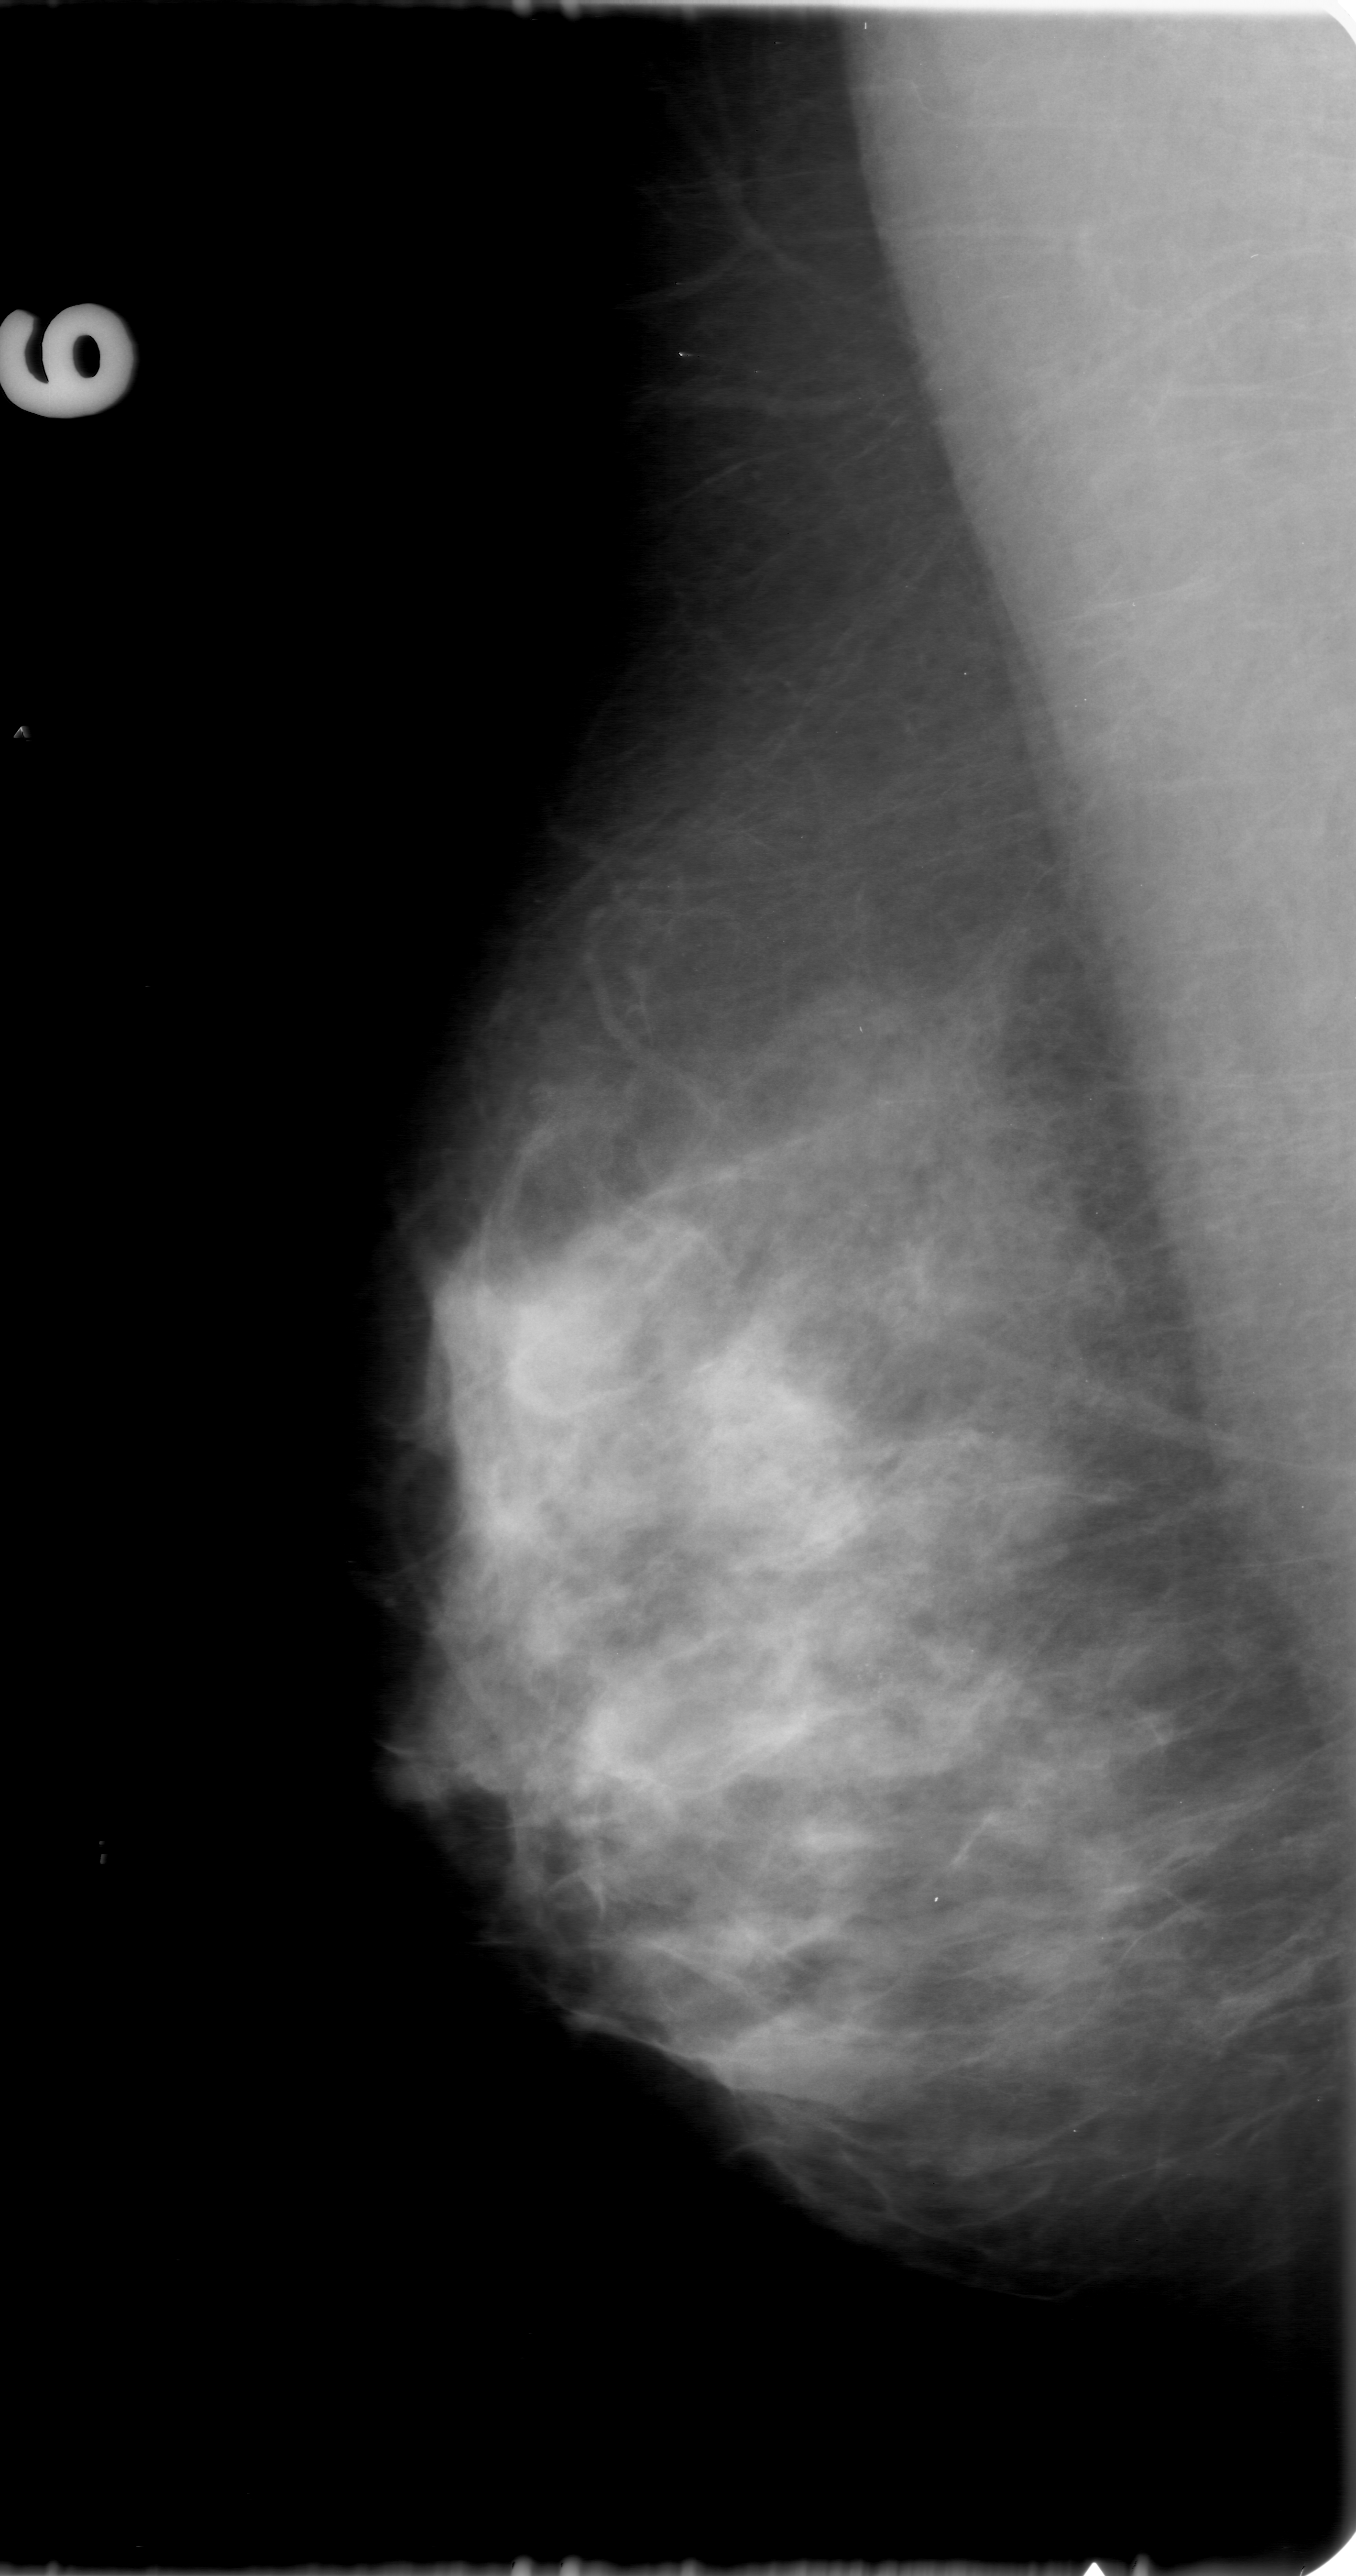
Digitized screen-film mammogram, right breast, MLO view, breast composition: heterogeneously dense (BI-RADS density category 3 of 4).
Marked findings (only marked abnormalities are described; nothing is implied about the rest of the image): calcifications, morphology amorphous, distribution clustered; BI-RADS assessment category 3; pathology (as recorded): malignant.